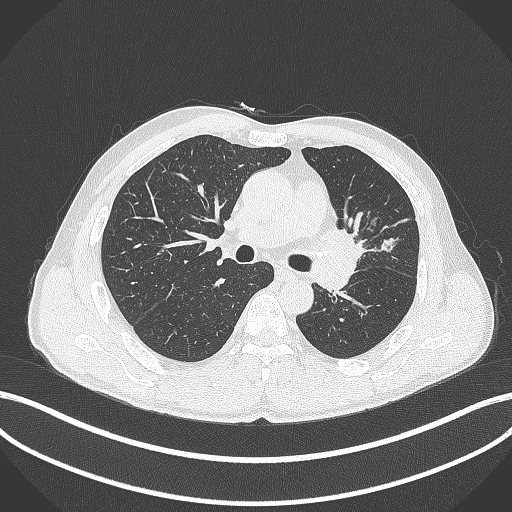
Chest CT, one axial slice; slice 254 of 429 in the series (ordered by position); reconstruction kernel B70f; lung window (W 1500 / L -600 HU); 1 mm slice thickness; 512 × 512 image matrix. Male patient, age 57 years. From the clinical record (not read from this slice): clinical TNM (as recorded): T2b N0 M0.
Structures marked on this image (bounding box drawn by a radiologist):
- lung tumour (recorded histology: squamous cell carcinoma): bounding box (x1, y1, x2, y2) in pixels: (314, 220, 372, 265)